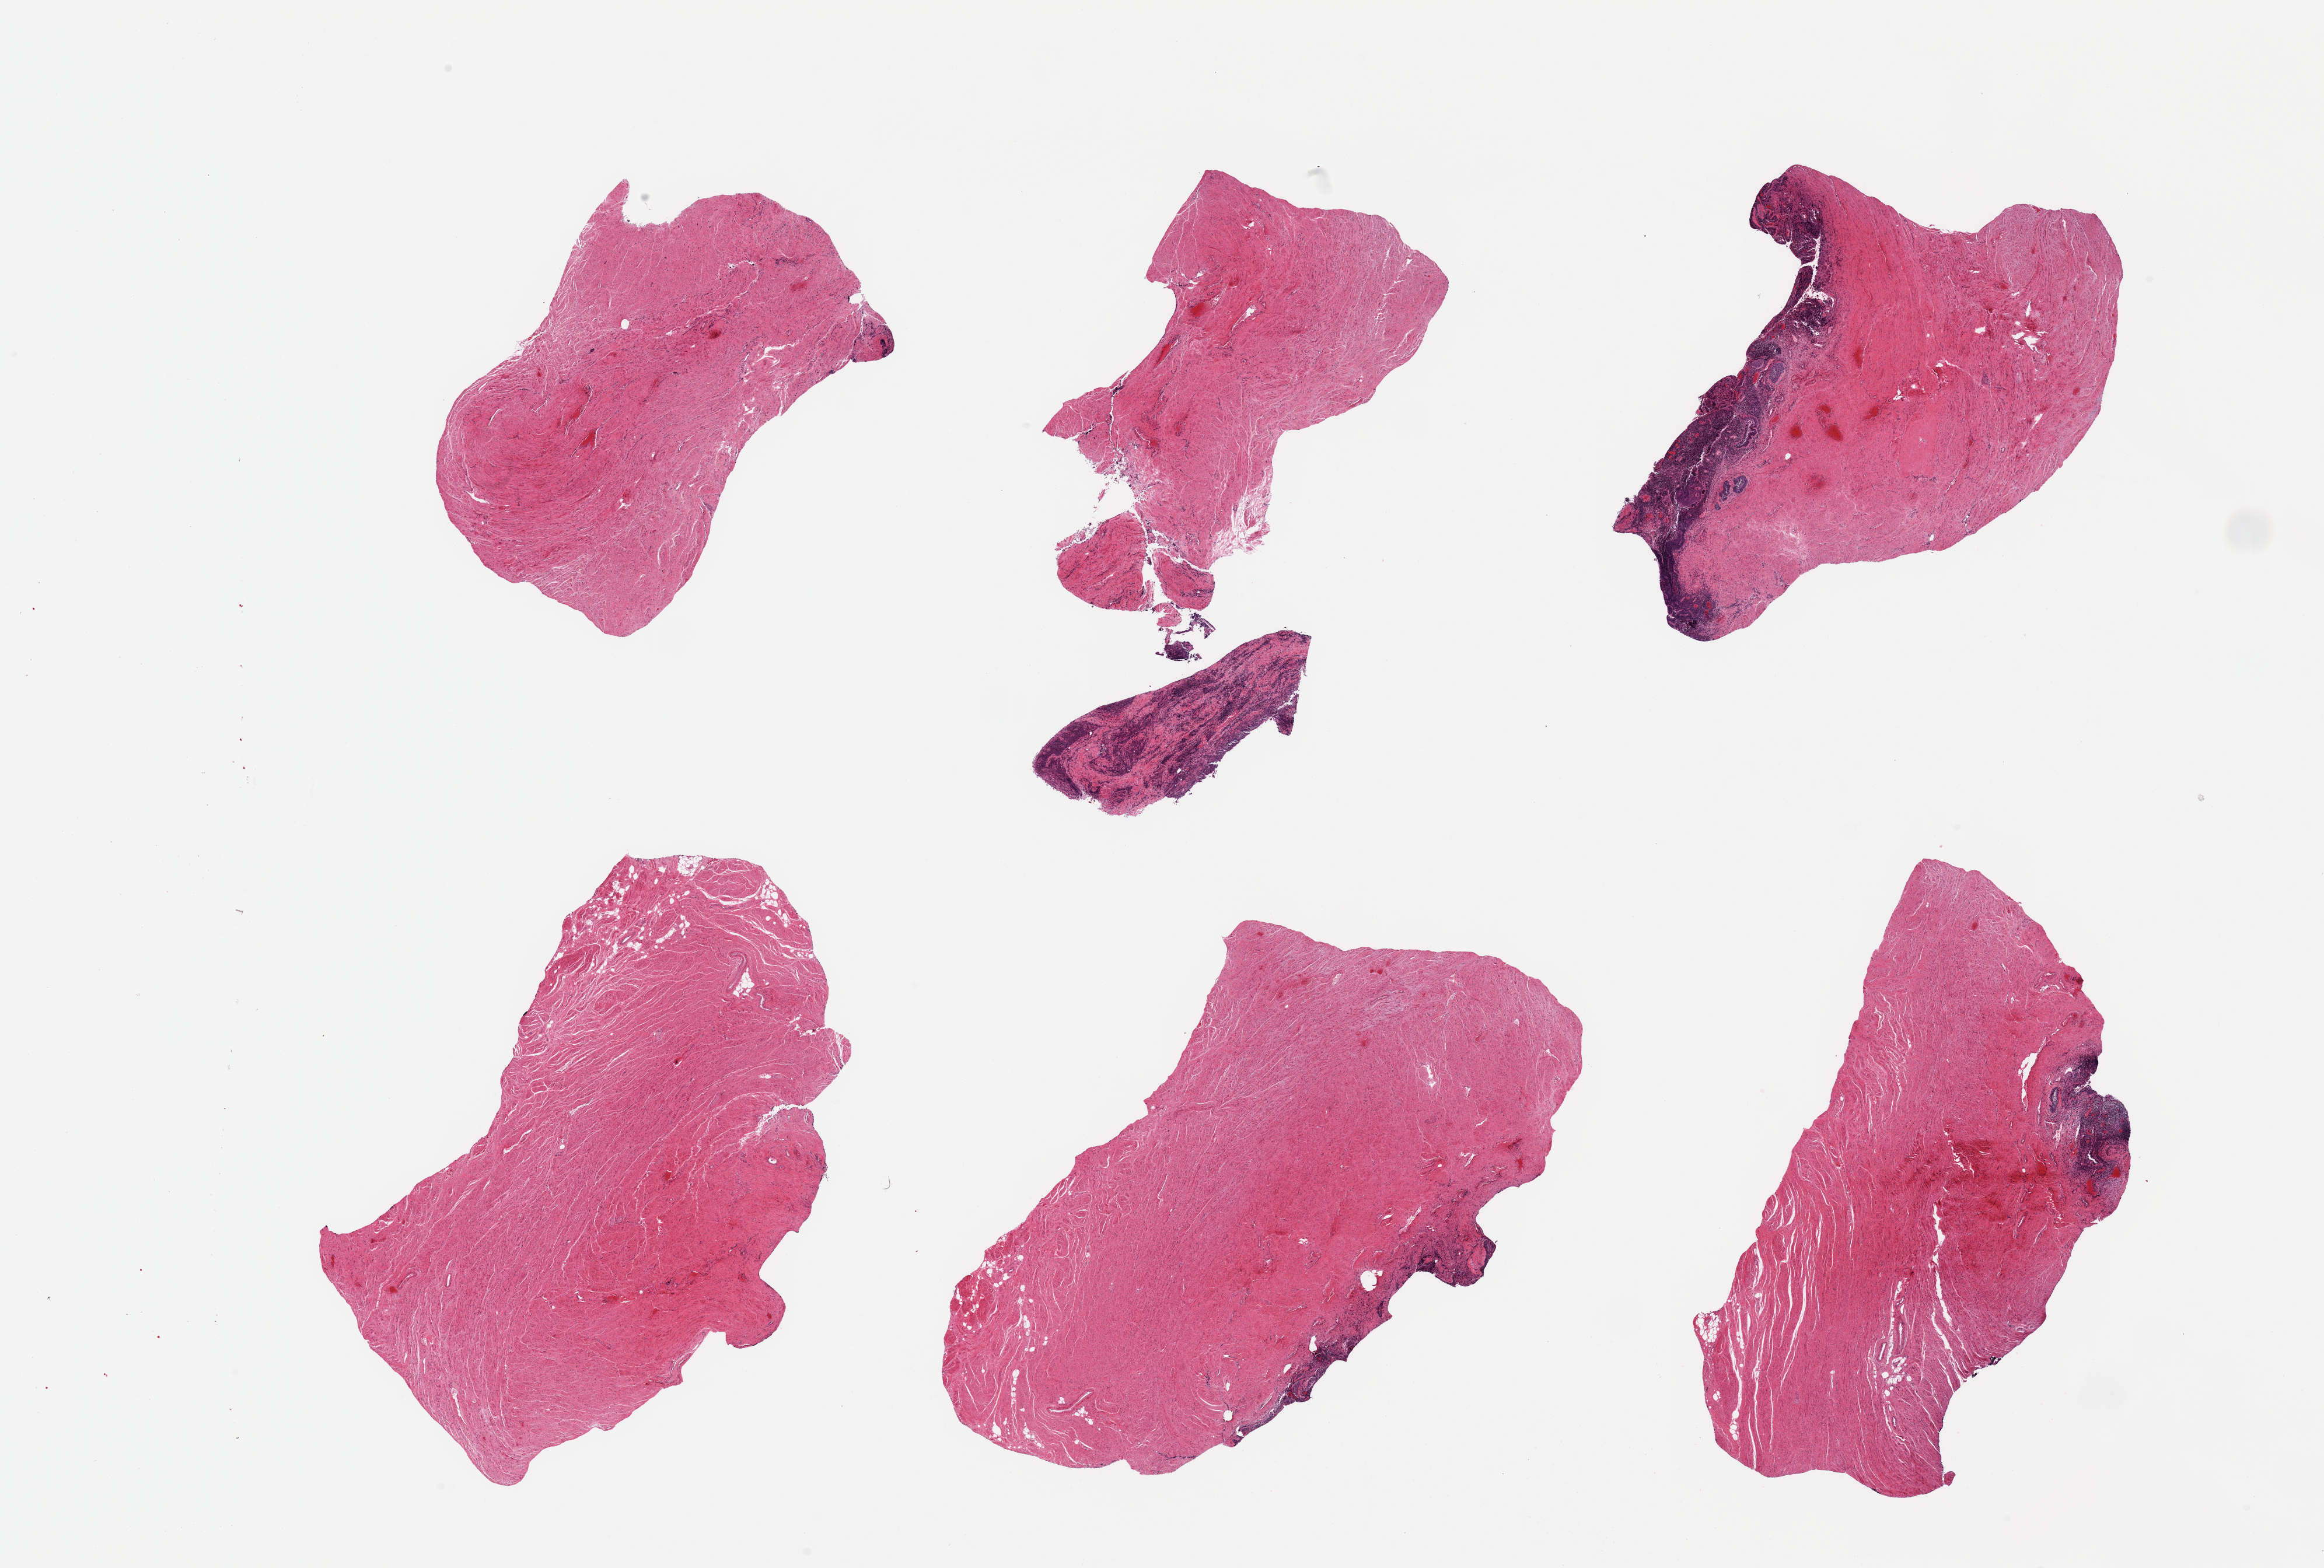
H&E whole-slide image — whole scanned area (about 31.5 x 21.3 mm) shown as a low-resolution overview, PAXgene-fixed, paraffin-embedded tissue, sampled site (target tissue): vagina, tissue donor sample. Donor: female.
Pathologist's review note for this sample: 6 pieces; mucosa largely sloughed; marked chronic inflammation and reactive atypia in remaining epithelium.